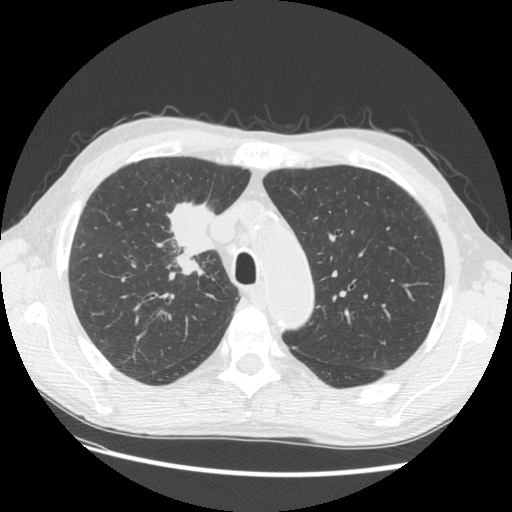
Low-dose screening chest CT, one axial slice; position 100 of 133 along the scan axis; lung window (W 1500 / L -600 HU); 2.5 mm slice thickness; 512 × 512 image matrix, field of view 360 × 360 mm.
Structures marked on this image (manually delineated by an expert):
- lesion 1 (tumor, hilum of right lung): bounding box [x1, y1, x2, y2] px = [166, 201, 218, 276]